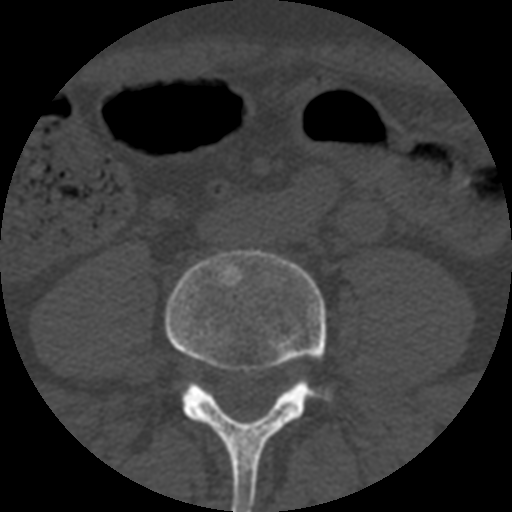
CT including the spine, one axial slice. Position 88 of 508 along the scan axis. Reconstruction kernel STANDARD. Bone window (W 1800 / L 400 HU). 1.25 mm slice thickness. 512 × 512 image matrix. Patient age 57 years. Case-level facts recorded for this patient, not image findings: primary cancer: prostate.
Structures marked on this image (semi-automatic segmentation, software-assisted and operator-edited):
- L4 vertebra: bounding box <166,250,332,512> (left, top, right, bottom; pixels)